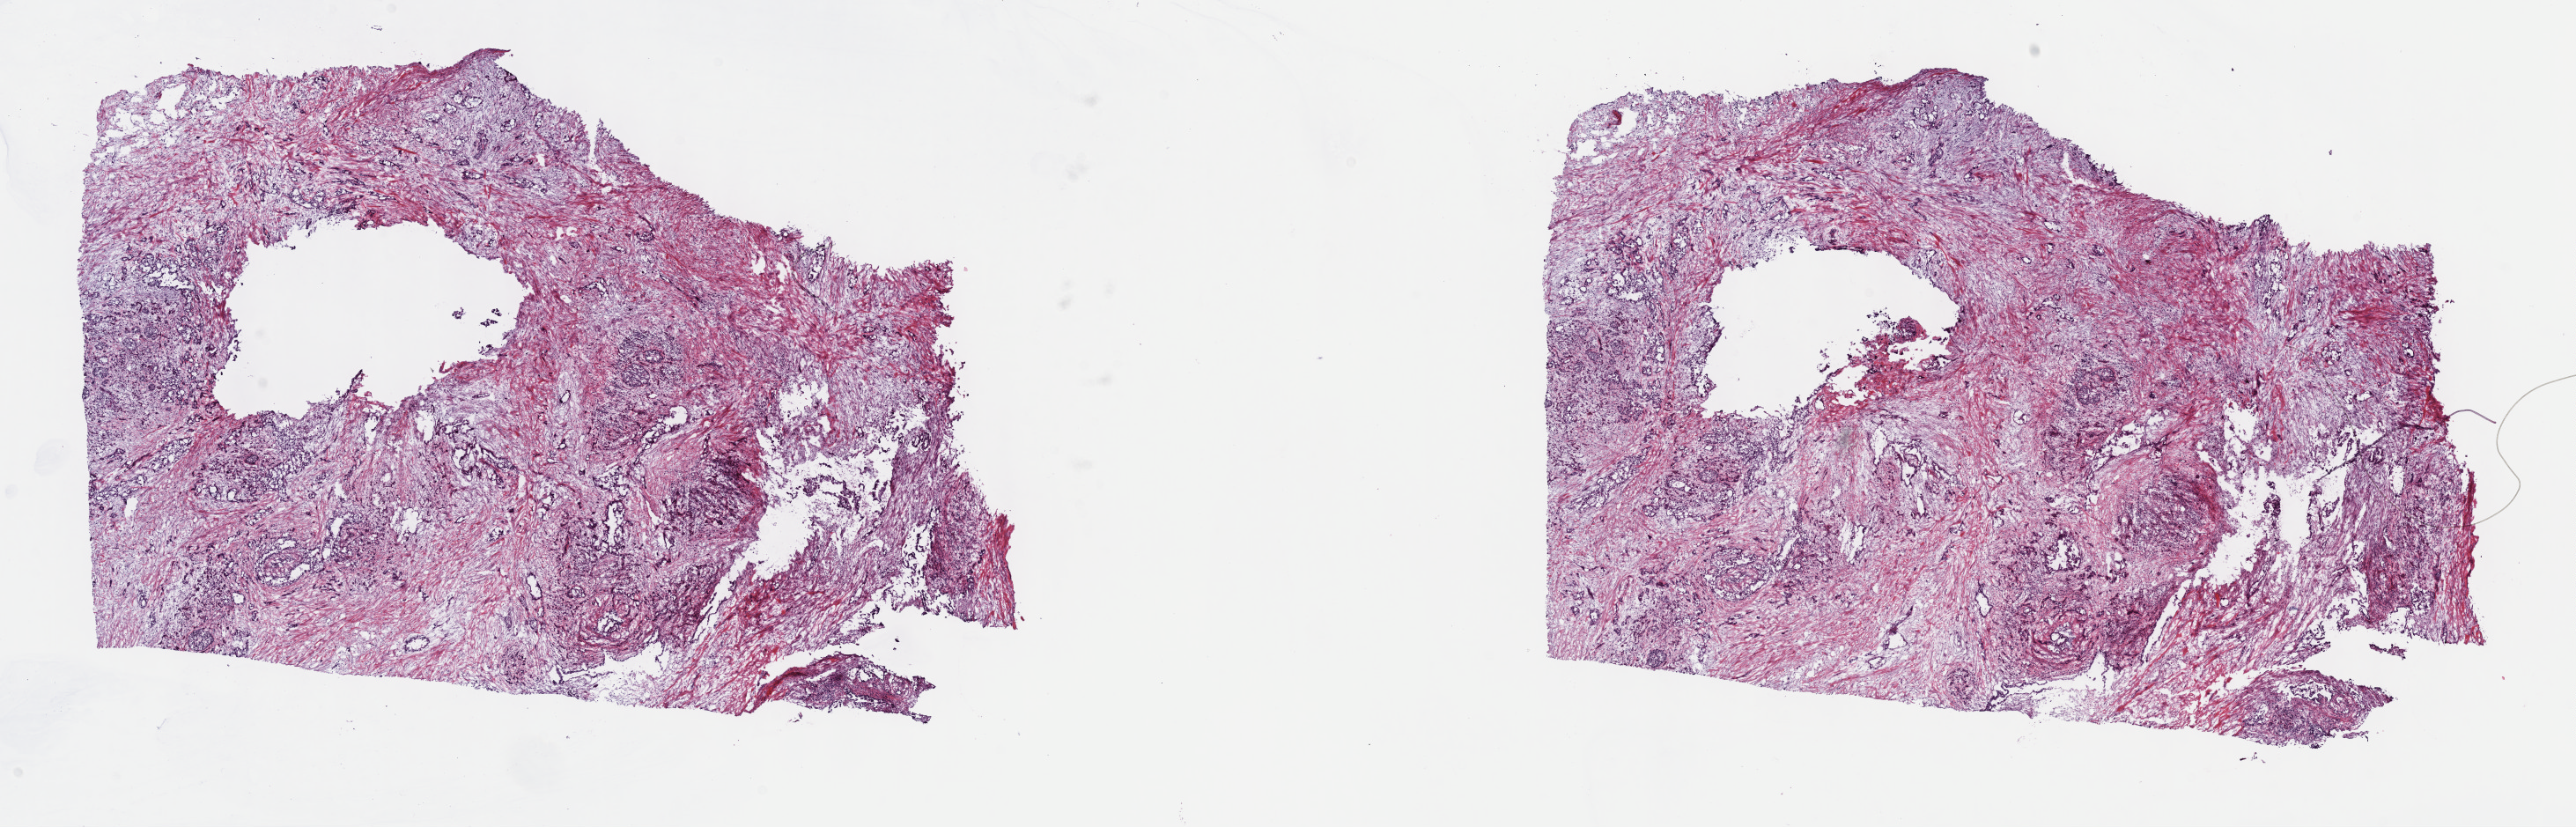
Whole-slide histology image, H&E — a low-resolution overview of the entire scanned area, about 23.7 x 7.6 mm. Frozen section from the top of the tissue portion. Primary tumour sample from the bile duct. Patient: female, age at initial diagnosis 70 years. Histologic grade: G1 (well differentiated). Slide review estimates, as recorded: tumour cells 100%, tumour nuclei 70%, normal cells 0%, stromal cells 0%, necrosis 0%. Inflammatory infiltration, as recorded: lymphocyte infiltration 5%, monocyte infiltration 0%, neutrophil infiltration 0%.
- histologic diagnosis: Cholangiocarcinoma
- AJCC pathologic stage: IVB (7th edition)